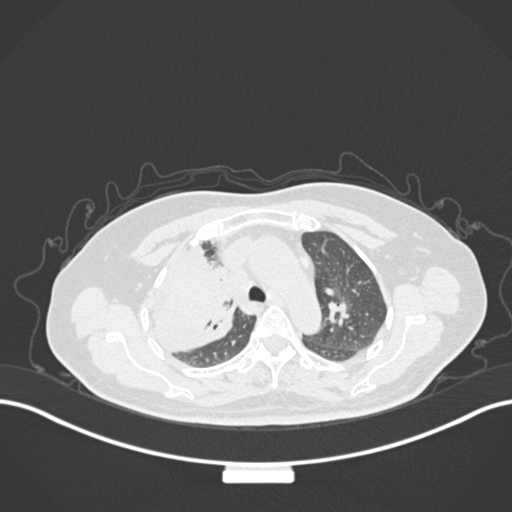
Chest CT, one axial slice; position 113 of 177 along the scan axis; reconstruction kernel B30f; lung window (W 1500 / L -600 HU); 1 mm slice thickness; 512 × 512 image matrix, field of view 400 × 400 mm. Female patient, age 60 years. From the clinical record (not read from this slice): clinical TNM (as recorded): T3 N1 M1.
Annotated regions visible in this slice (rectangle marked by the reading radiologist):
- lung tumour (recorded histology: adenocarcinoma): bounding box [x1, y1, x2, y2] px = [140, 234, 240, 357]